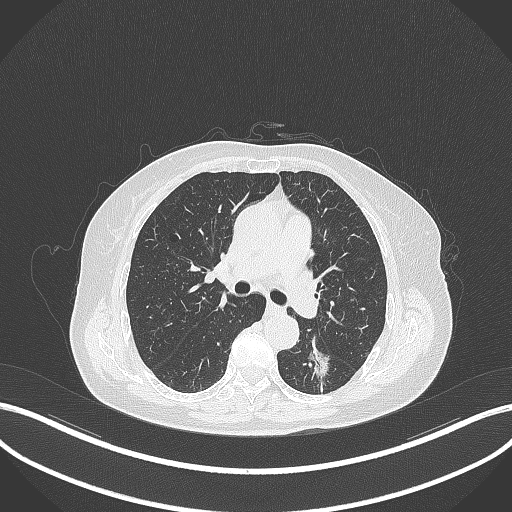
Chest CT, one axial slice; slice 179 of 352 in the series (ordered by position); reconstruction kernel B70f; lung window (W 1500 / L -600 HU); 1 mm slice thickness; 512 × 512 image matrix, field of view 400 × 400 mm. Patient: female, 70 years. Case-level facts recorded for this patient, not image findings: clinical TNM (as recorded): T1c N0 M0.
Structures marked on this image (rectangle marked by the reading radiologist):
- lung tumour (recorded histology: adenocarcinoma): bounding box <299,331,335,386> (left, top, right, bottom; pixels)